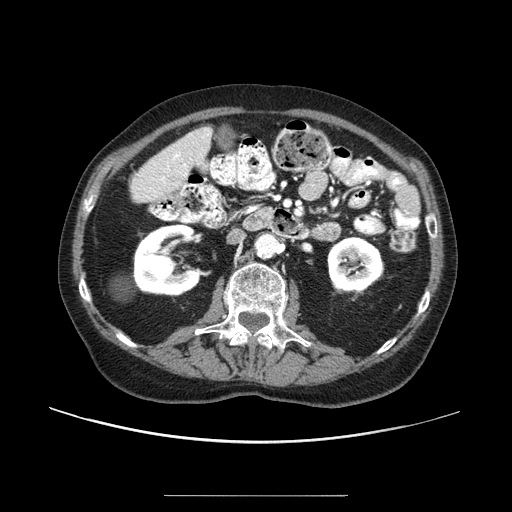
Contrast-enhanced abdominal CT (liver protocol), one axial slice; position 30 of 91 along the scan axis; 100 kVp; one of 2 acquisitions stored at this slice position; soft-tissue window (W 400 / L 40 HU); 512 × 512 image matrix. Case-level facts recorded for this patient, not image findings: diagnosis: hepatocellular carcinoma (patient treated with transarterial chemoembolisation; whether this scan precedes or follows treatment is not stated here); TNM stage (as recorded): Stage-I; Child-Pugh class: A.
Outlined on this slice (semi-automatically segmented with operator editing):
- liver parenchyma outside the tumour (the mass and vessels are separate outlines, so this box may not span the whole liver): bounding box <132,126,212,192> (left, top, right, bottom; pixels)
- liver vessels: <151,132,210,183>